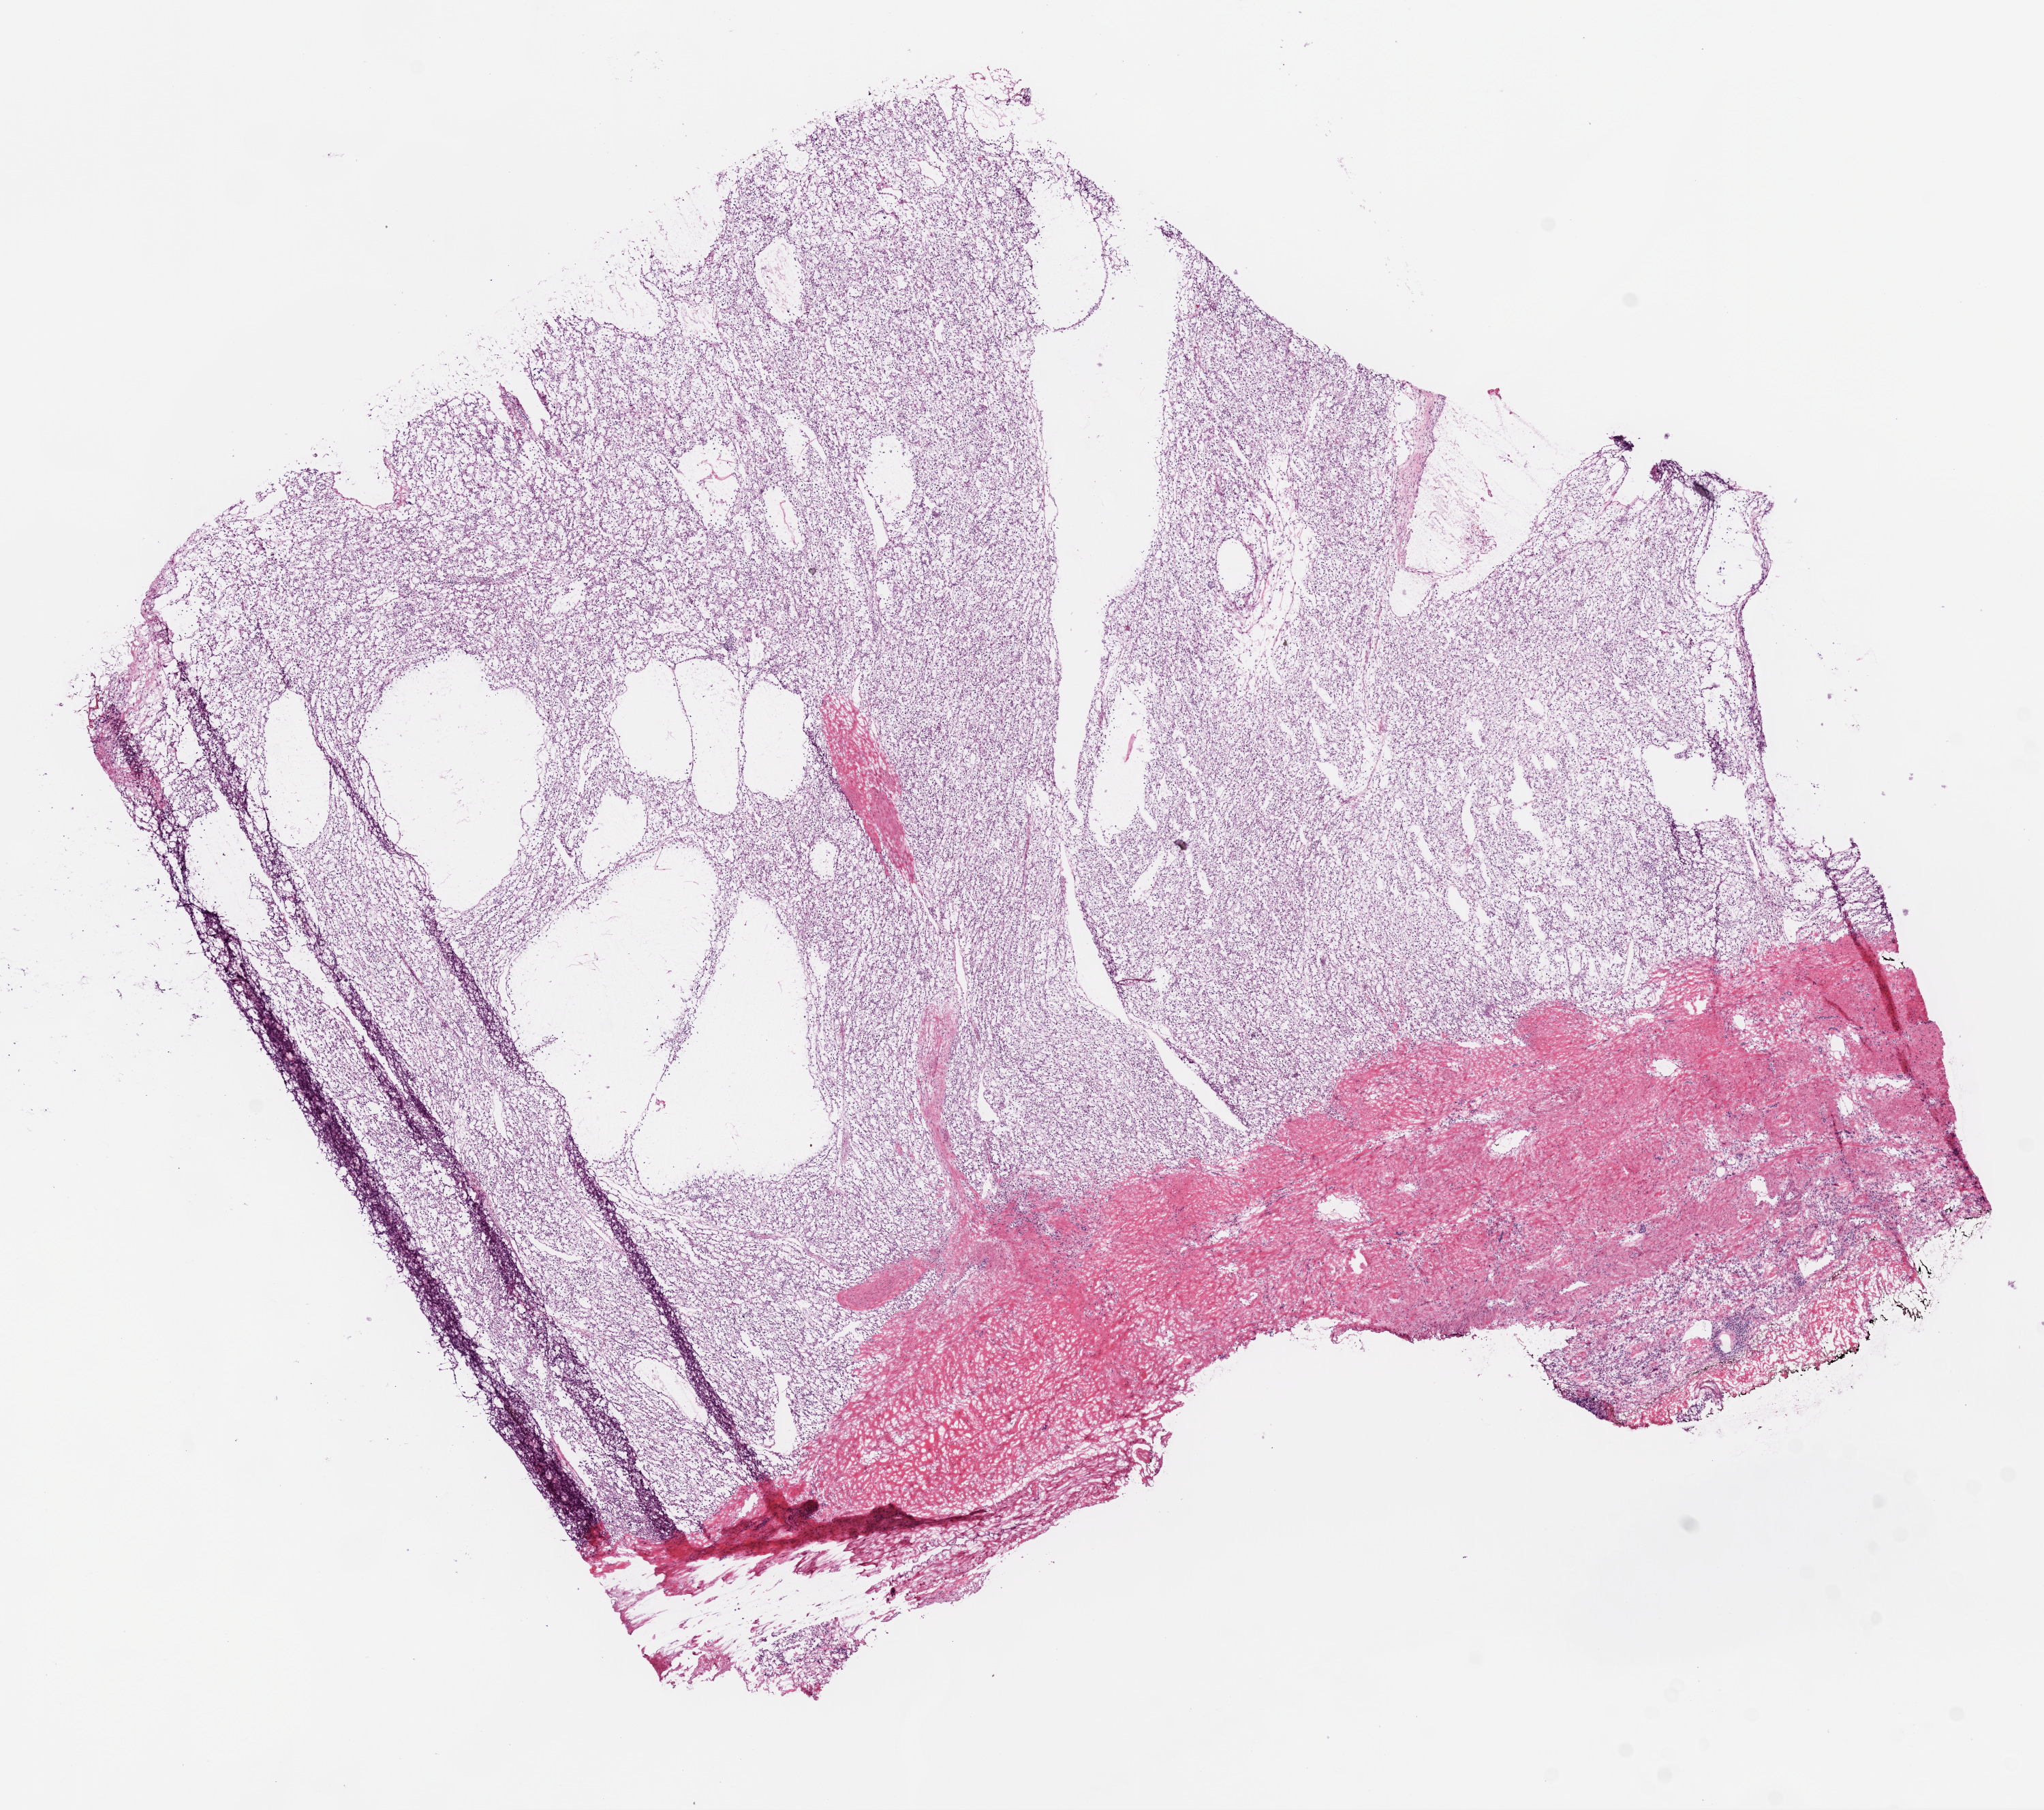
H&E-stained whole-slide image — shown as a low-resolution overview of the whole scanned area (about 12.0 x 10.7 mm, slide scanned at 20x), frozen section, primary tumour sample from the kidney. Female patient; age at initial diagnosis 48 years. Histologic grade: G2 (moderately differentiated). Composition of this section per pathologist review: tumour cells 80%, tumour nuclei 80%, normal cells 15%, stromal cells 5%, necrosis 0%.
* AJCC pathologic stage: I
* pathologic diagnosis: Clear cell adenocarcinoma, NOS